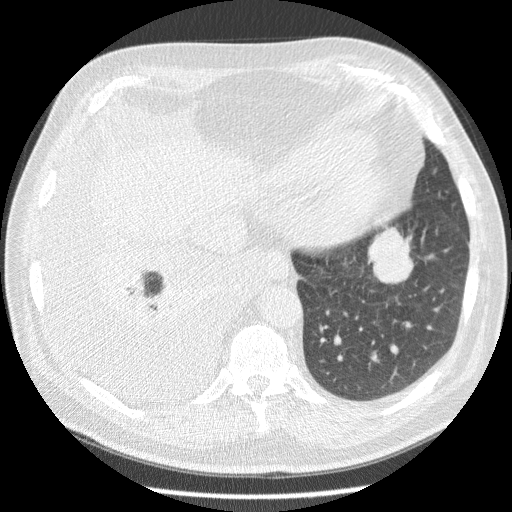
Low-dose screening chest CT, axial slice, third annual screen, lung window (W 1500 / L -600 HU), 2.5 mm slice thickness, standard (soft-tissue) reconstruction kernel (STANDARD). Male participant, aged 63 years at enrolment. Current smoker at enrolment.
Expert reader's lesion annotation, bounding box (x1, y1, x2, y2) in pixels: (357, 218, 421, 284). The exam's reader record, not a measurement of the box and not confirmed to be the same lesion: non-calcified nodule or mass ≥4 mm, left lower lobe, 34 × 31 mm, smooth margins, soft tissue attenuation, pre-existing on the prior screen: yes; interval growth: yes. Participant outcome: lung cancer diagnosed 30 days after this screen — squamous cell carcinoma, NOS, left lower lobe, stage IB (AJCC 6th edition), 48 mm at pathology.